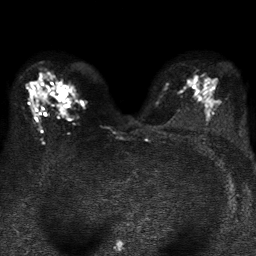
Breast MRI, one axial slice; slice 22 of 37 in the series (ordered by position); diffusion-weighted series; image 2 of 4 stored at this slice position (different b-values; order by instance number); 1.5 T; 5 mm slice thickness; 256 × 256 image matrix. Female patient.
Annotated regions visible in this slice (outlined manually by an expert reader):
- tumour on diffusion-weighted imaging: bounding box <57,86,67,99> (left, top, right, bottom; pixels)